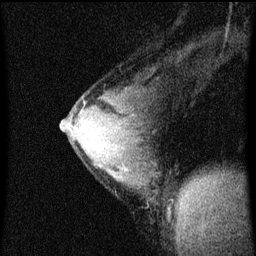
Breast MRI (dynamic contrast-enhanced), one sagittal slice. Position 38 of 60 along the scan axis. Dynamic contrast-enhanced series, image 2 of 4 at this slice position (ordered by acquisition). 1.5 T. TE 4.2 ms, TR 8 ms. 2 mm slice thickness. 256 × 256 image matrix, field of view 180 × 180 mm. Female patient, age 33 years.
Annotated regions visible in this slice (semi-automatically segmented with operator editing):
- analysis volume of interest (the breast-tissue region the enhancement analysis was run in; not a lesion): bounding box [x1, y1, x2, y2] px = [62, 80, 167, 205]
- tumour enhancement mask (voxels above the 70 % enhancement threshold inside the analysis volume of interest): [63, 122, 84, 149]